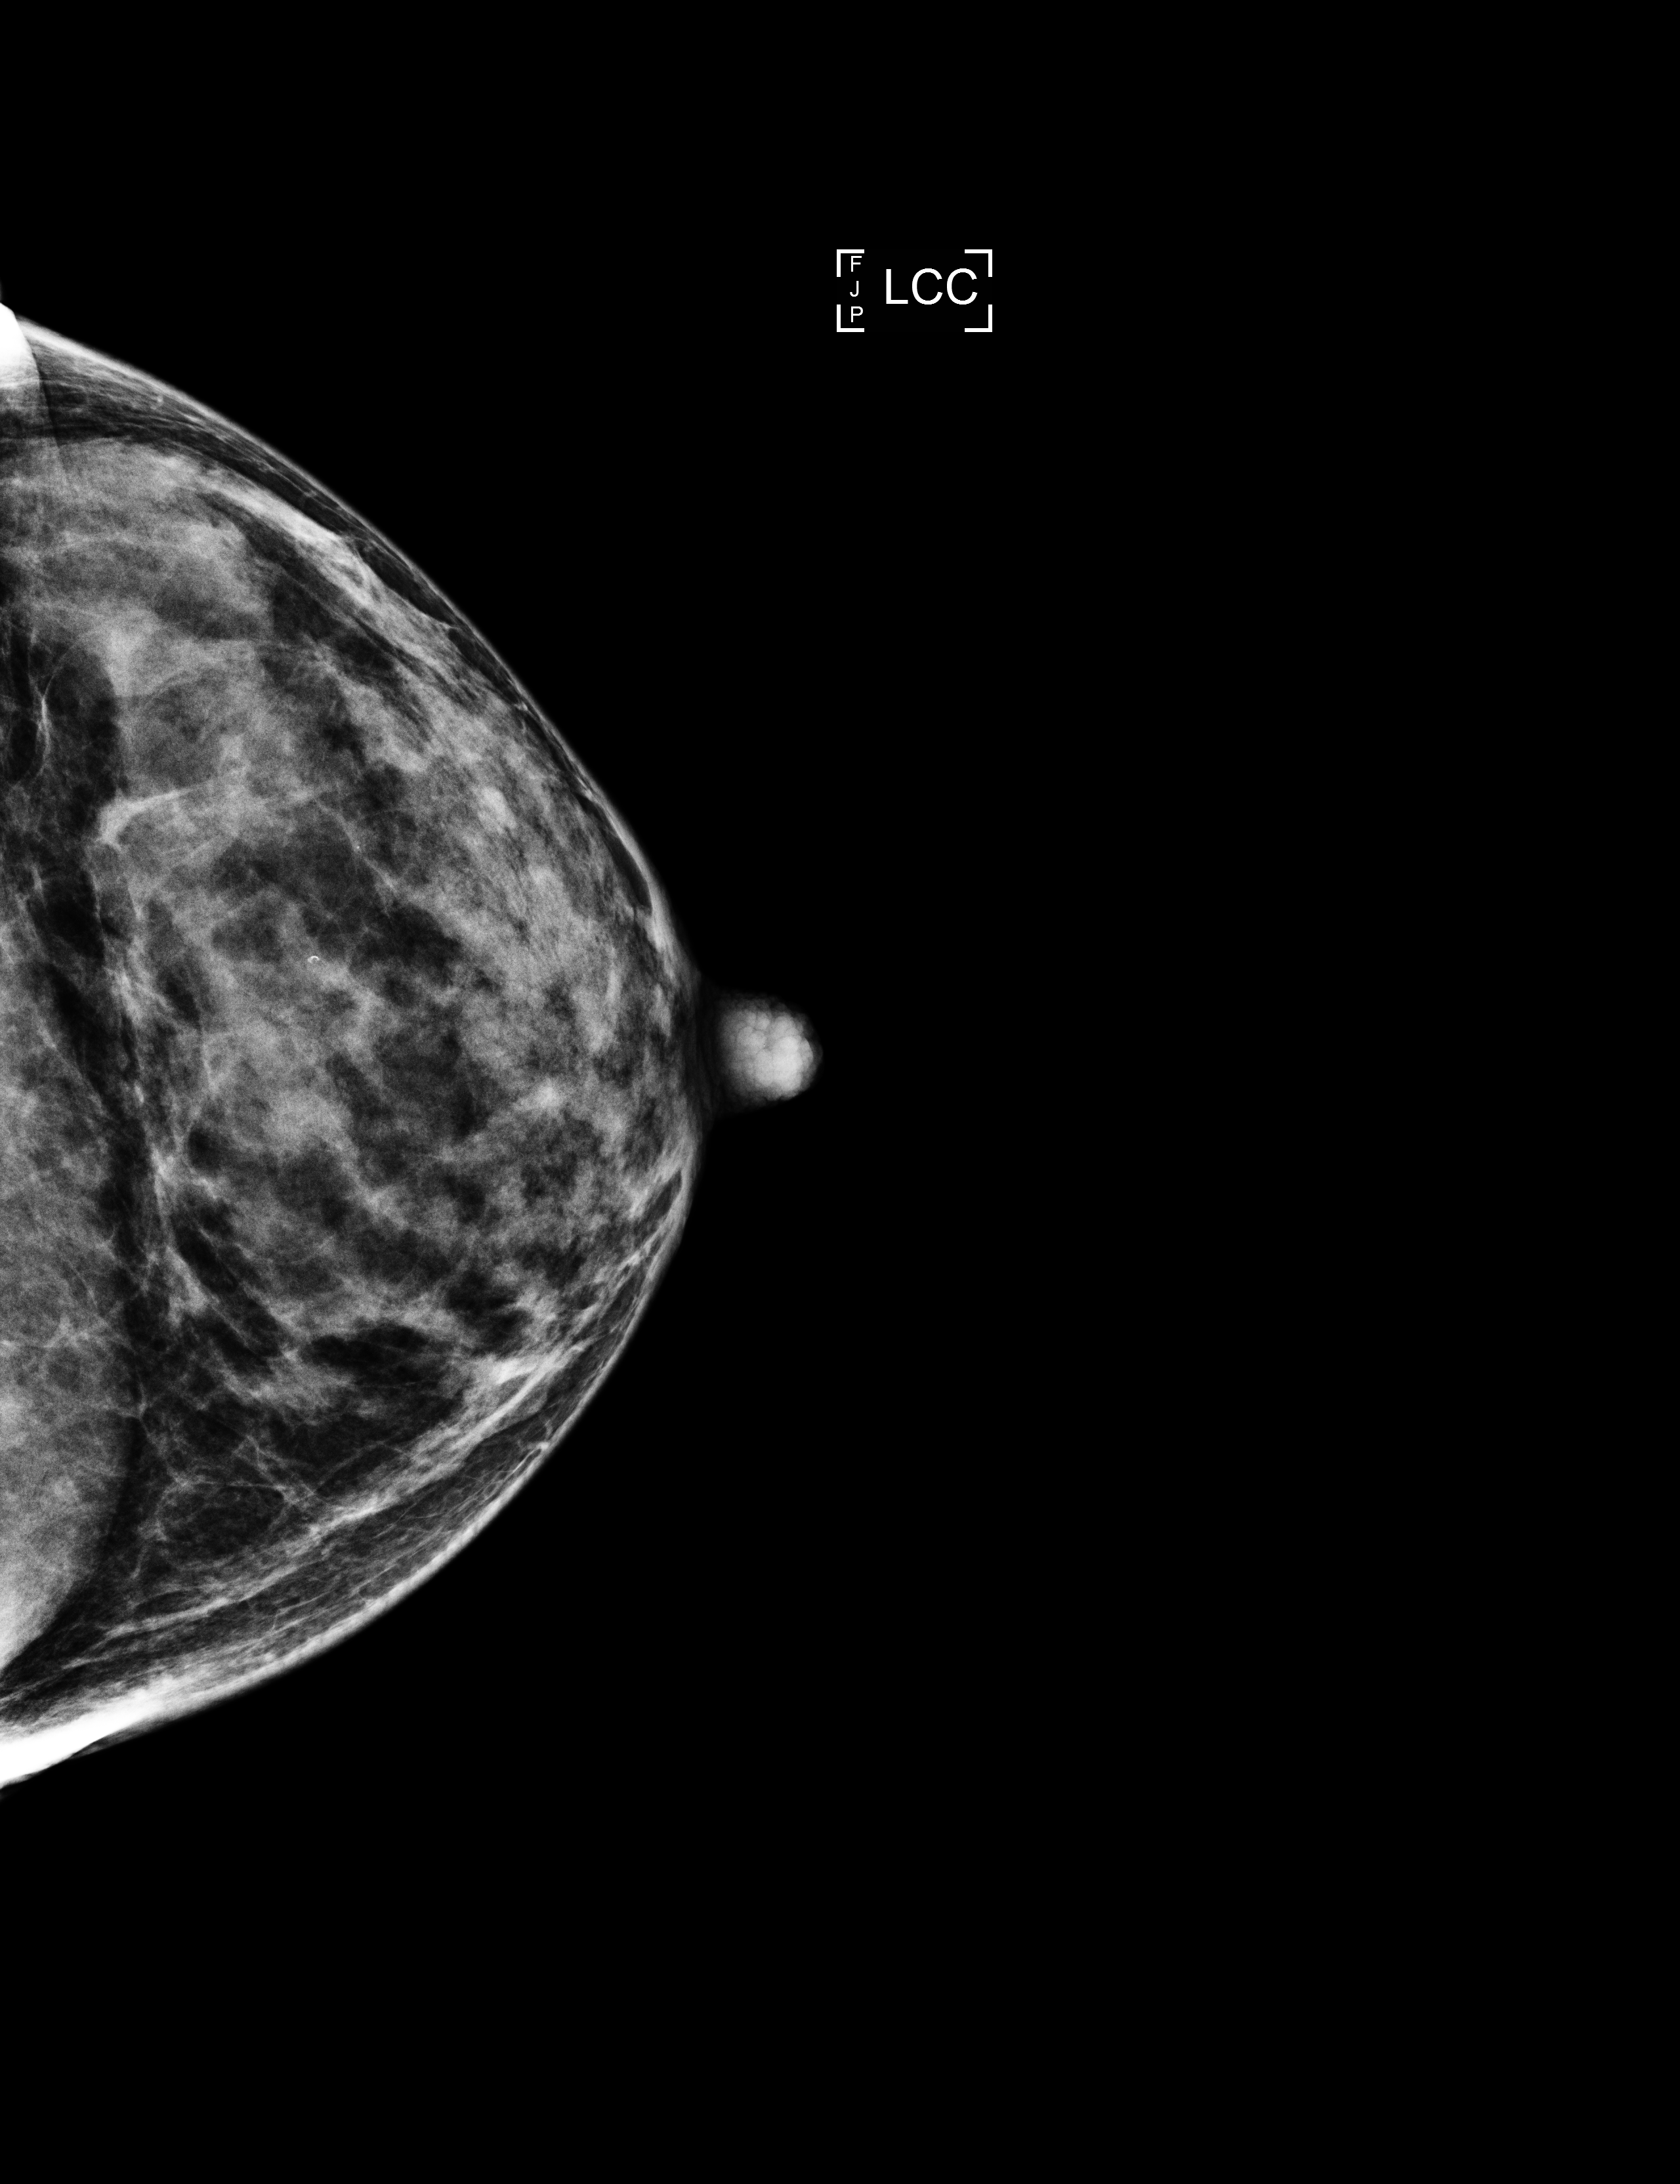
Full-field digital mammogram (FFDM); left breast; cranio-caudal projection; annual screening mammography examination; compressed breast thickness 38 mm. Patient aged 53 years (female).
- BI-RADS breast density category at the screening exam (both breasts, scale 1–4): 4
- final BI-RADS category for the screening round (tomosynthesis exam, both breasts): category 2
- recall: no recall after this screen